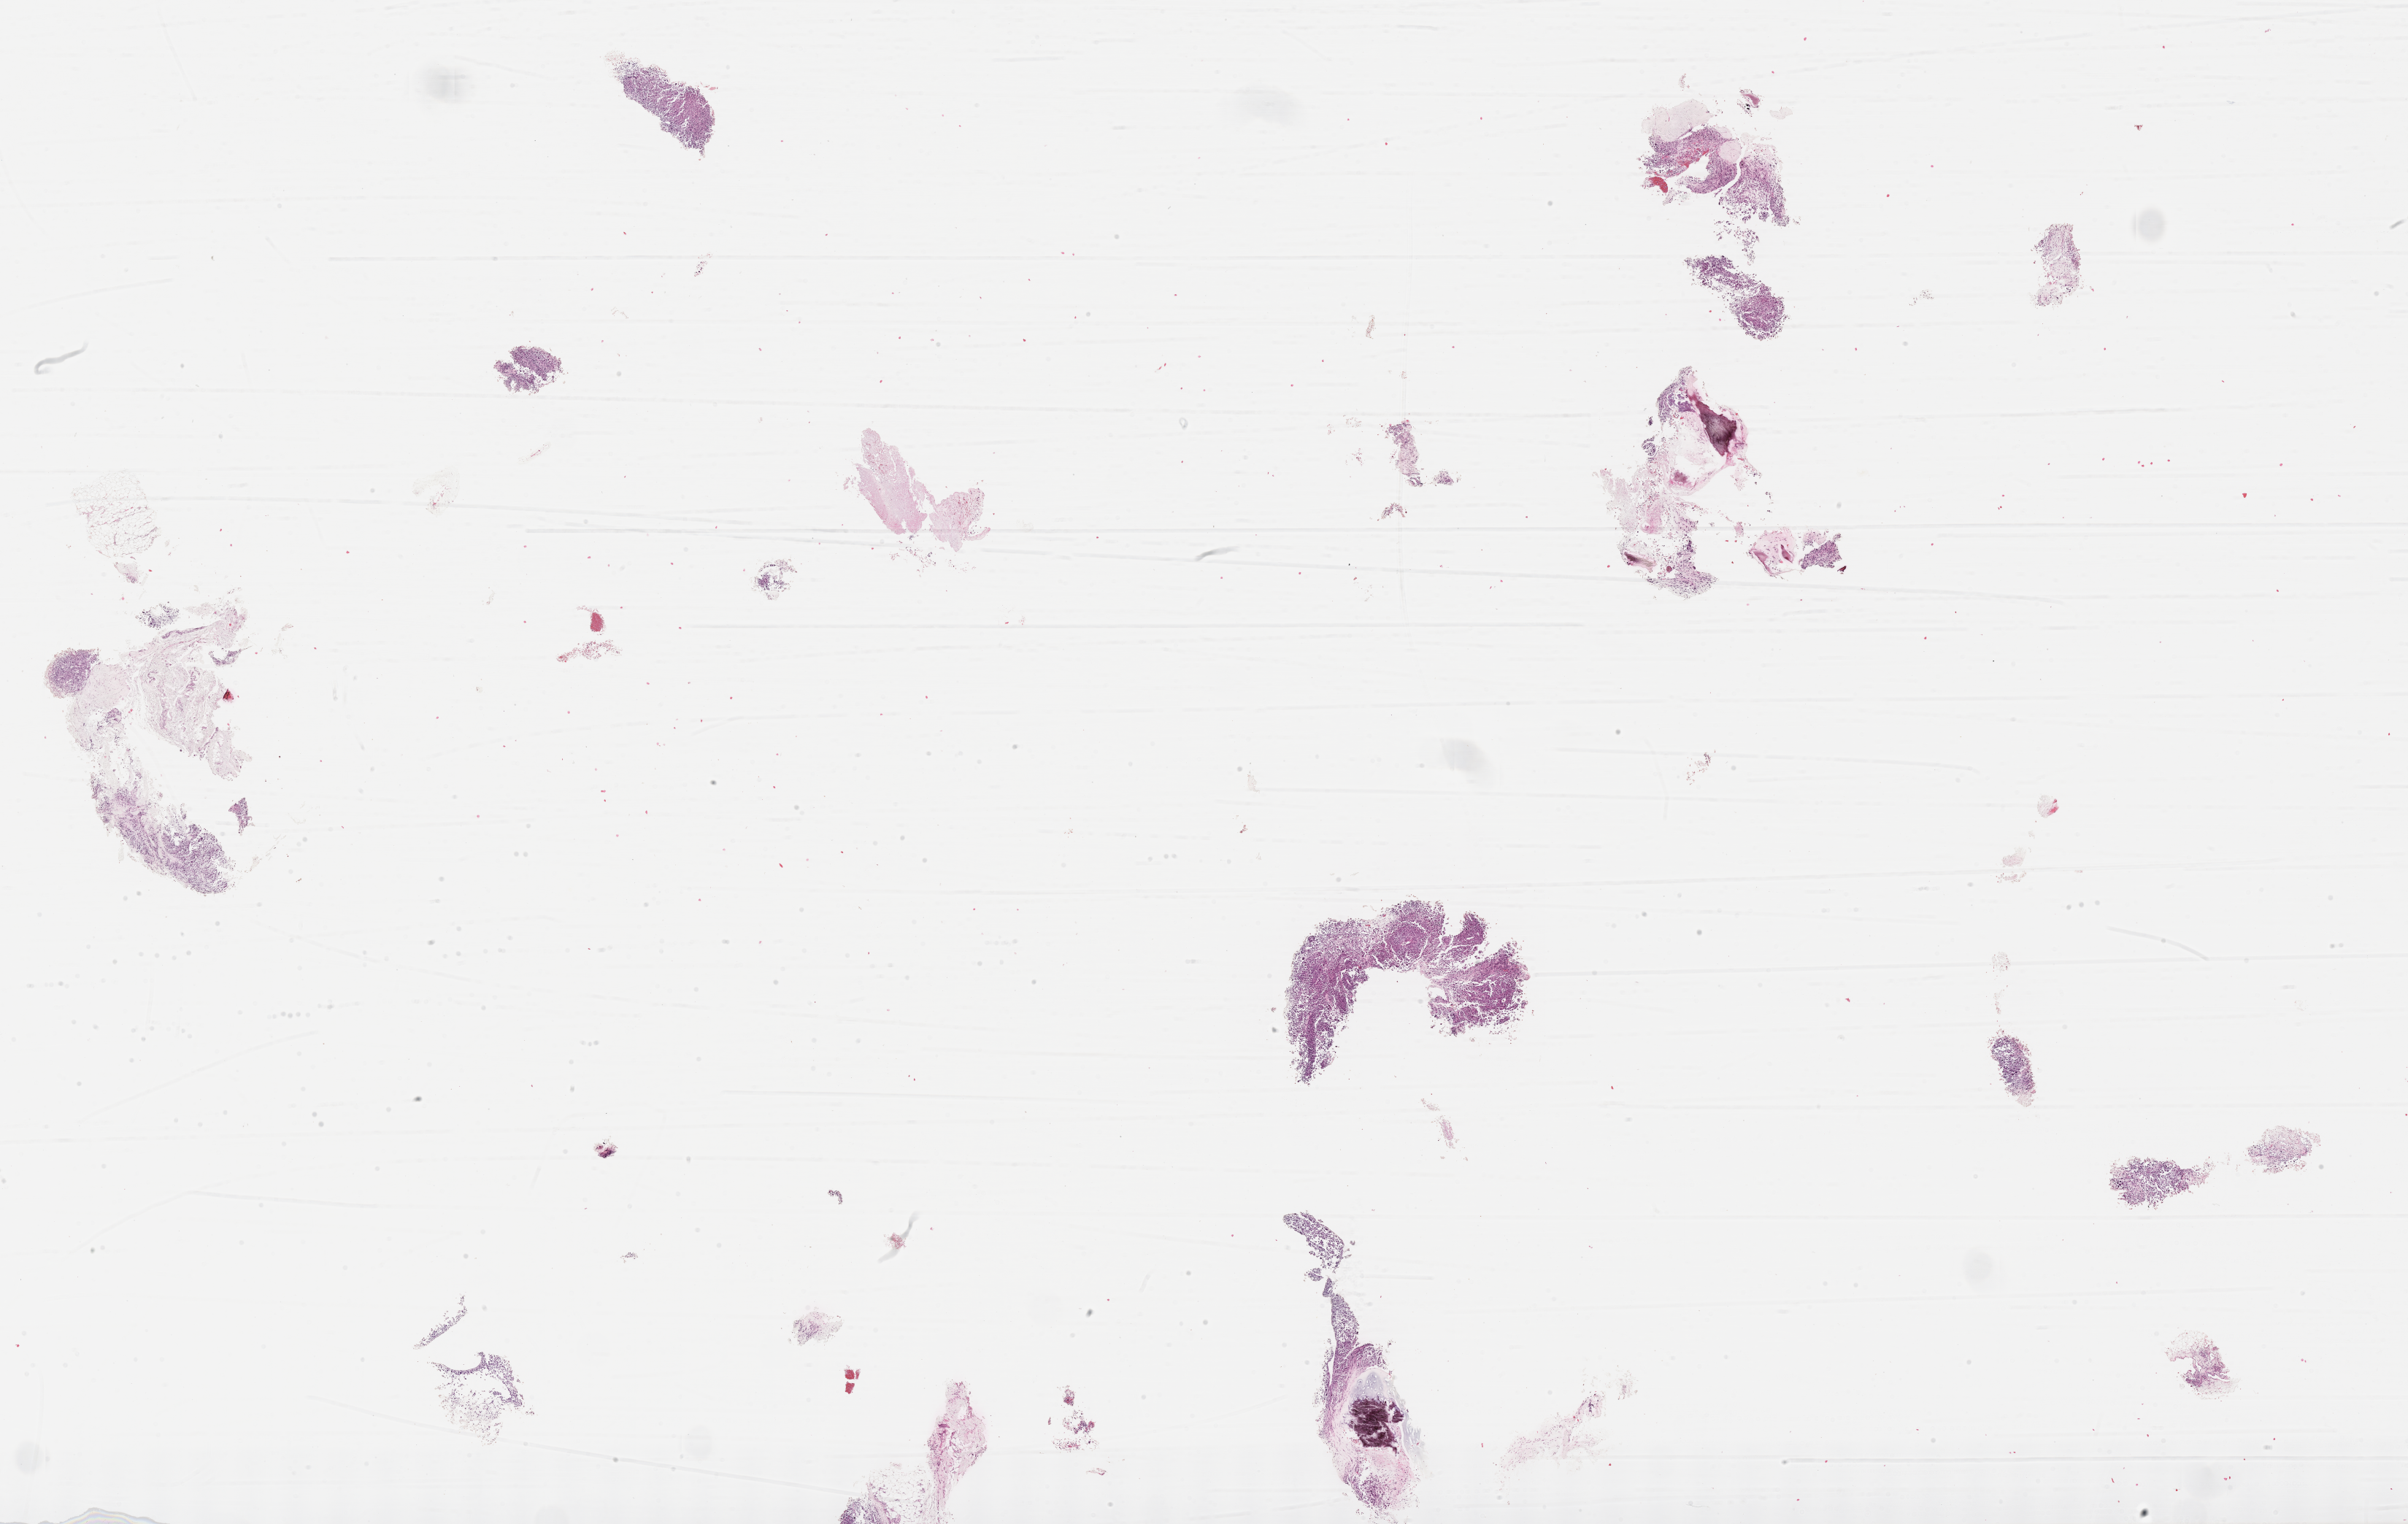
Whole-slide image, haematoxylin and eosin stain of tumor tissue — low-resolution overview of the scanned area, about 26.7 x 16.9 mm; formalin-fixed, paraffin-embedded (FFPE) tissue; sample anatomic site: pelvis. Patient: female, age 16.8 years at diagnosis.
Diagnosis: rhabdomyosarcoma; histological classification: alveolar rhabdomyosarcoma. Metastatic status at presentation (as recorded): non-metastatic (unconfirmed).